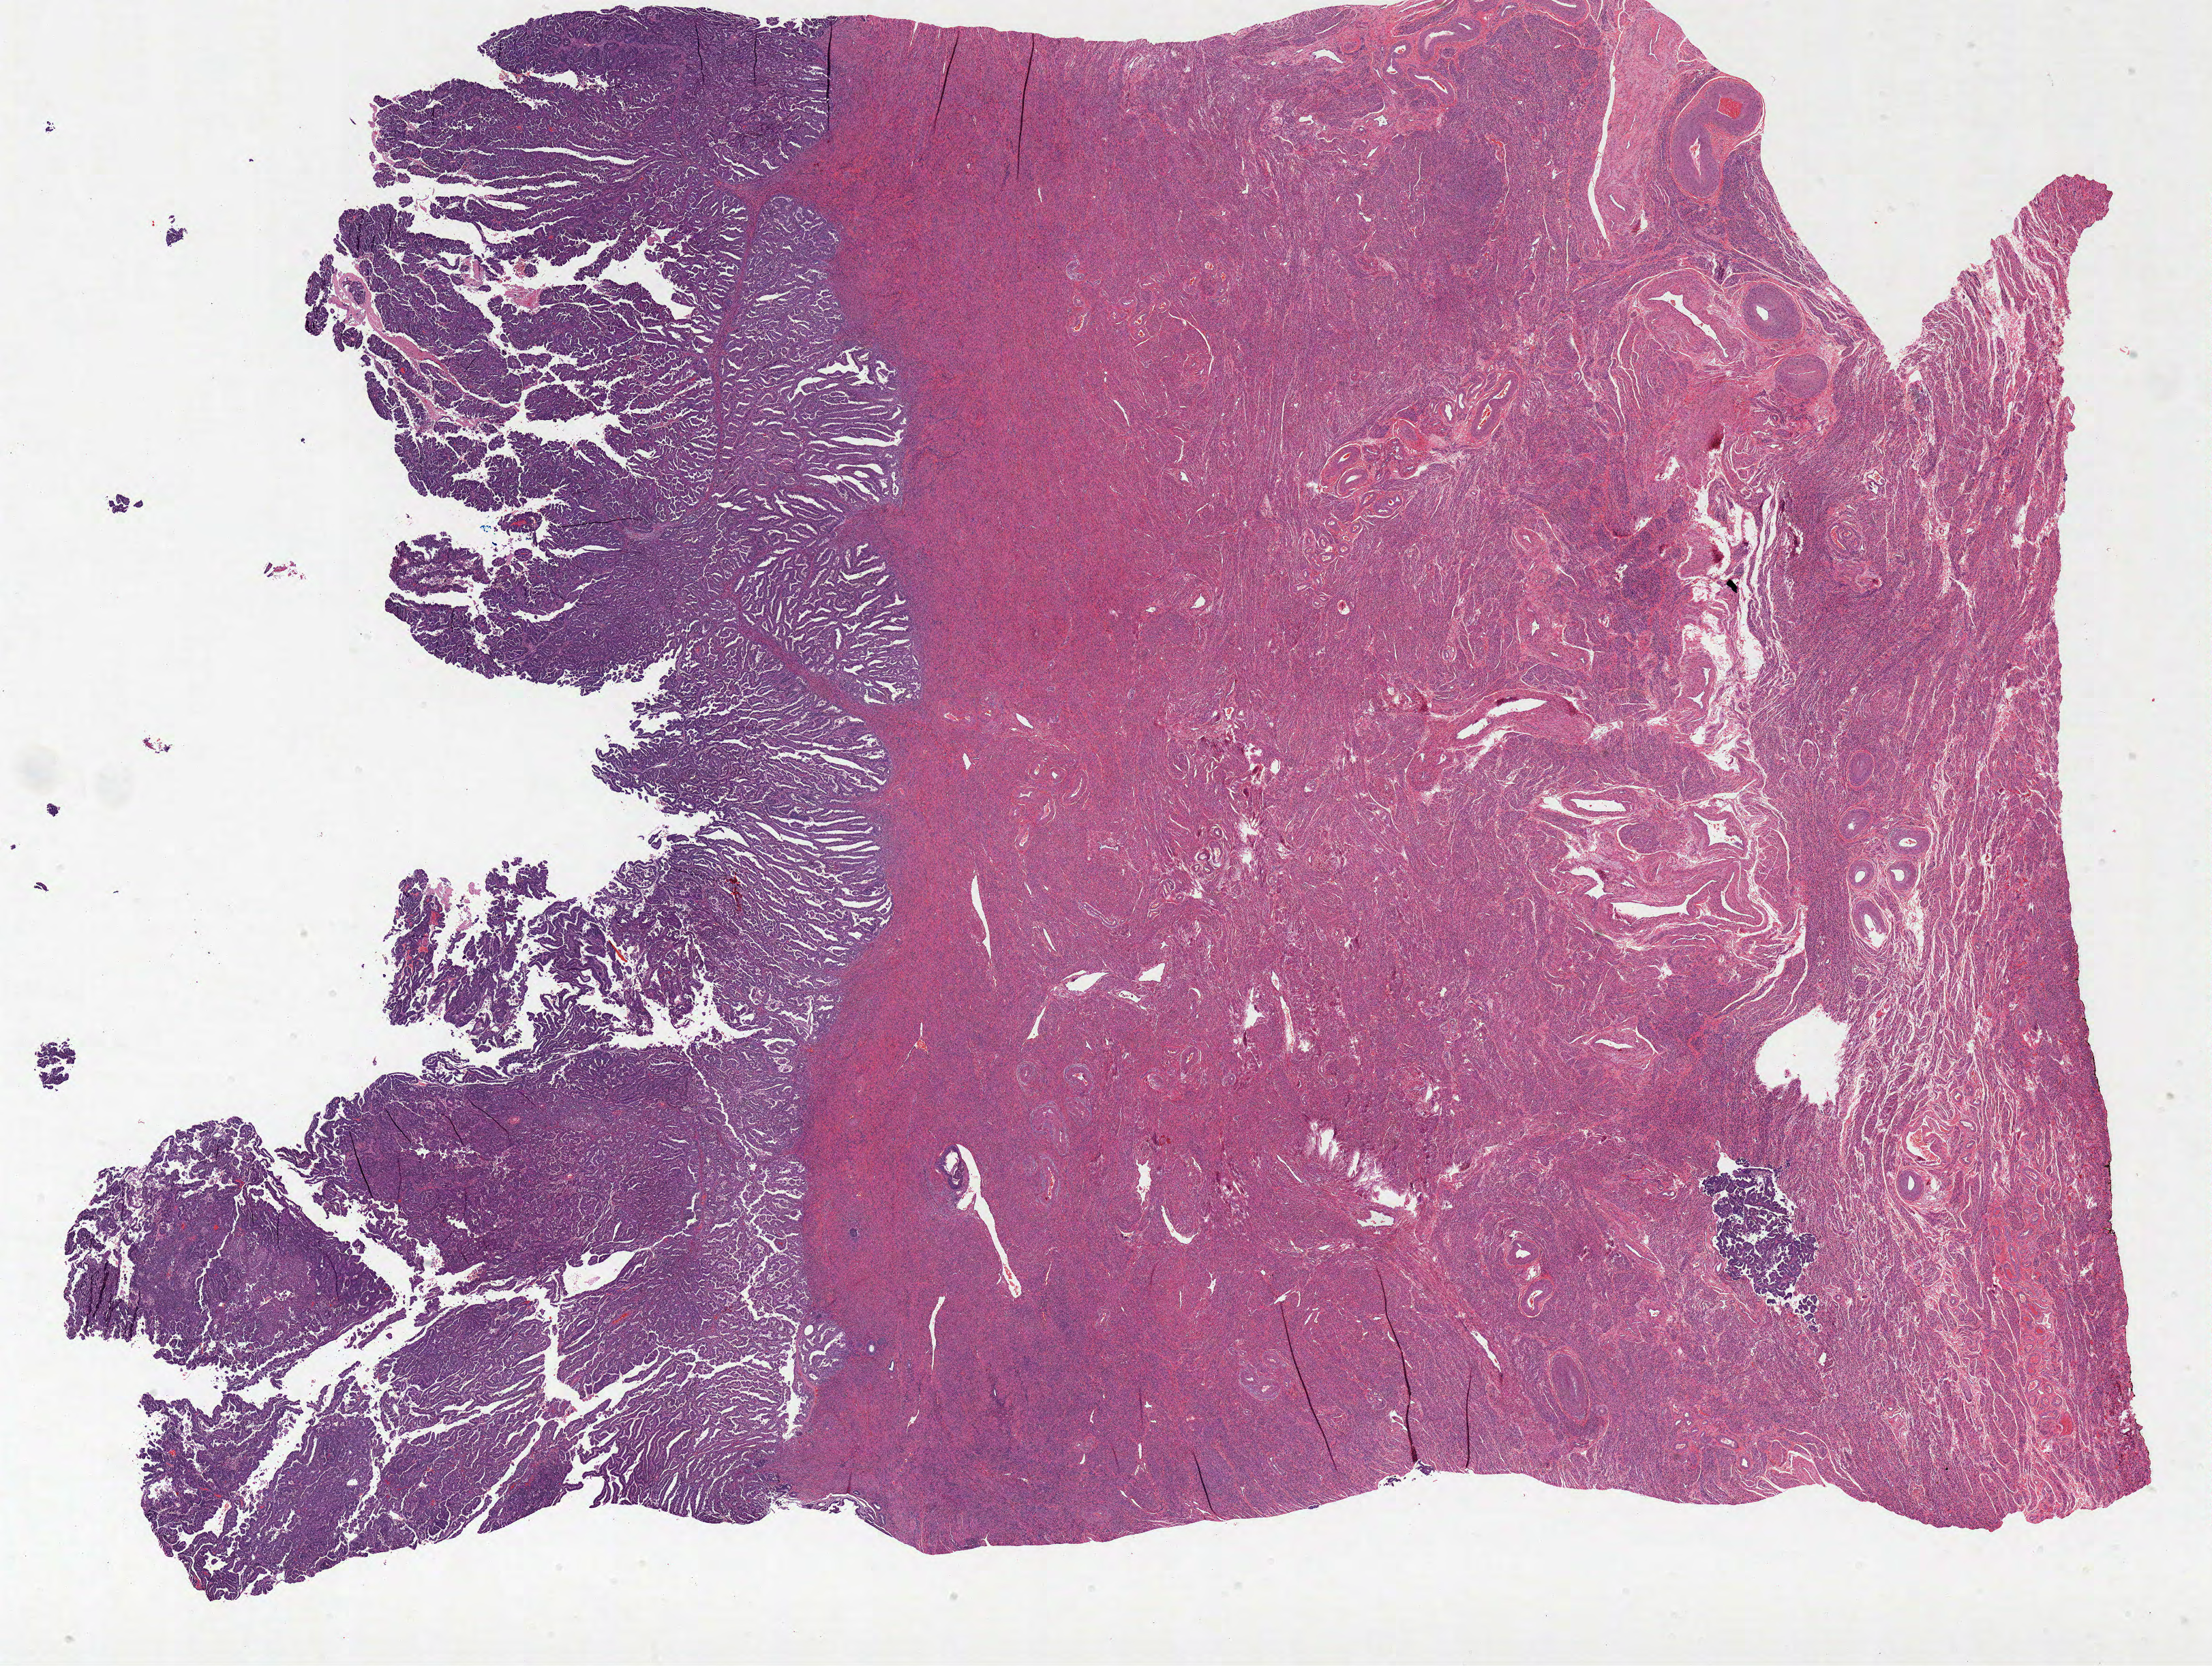
Digitized H&E-stained tissue section (whole slide) — low-resolution overview of the scanned area, about 25.9 x 19.5 mm, formalin-fixed paraffin-embedded (FFPE) diagnostic section, primary tumour sample from the uterus. Female, age 66 years at initial diagnosis. Histologic grade: G3 (poorly differentiated).
- FIGO stage: II
- diagnosis: Serous cystadenocarcinoma, NOS (endometrium)